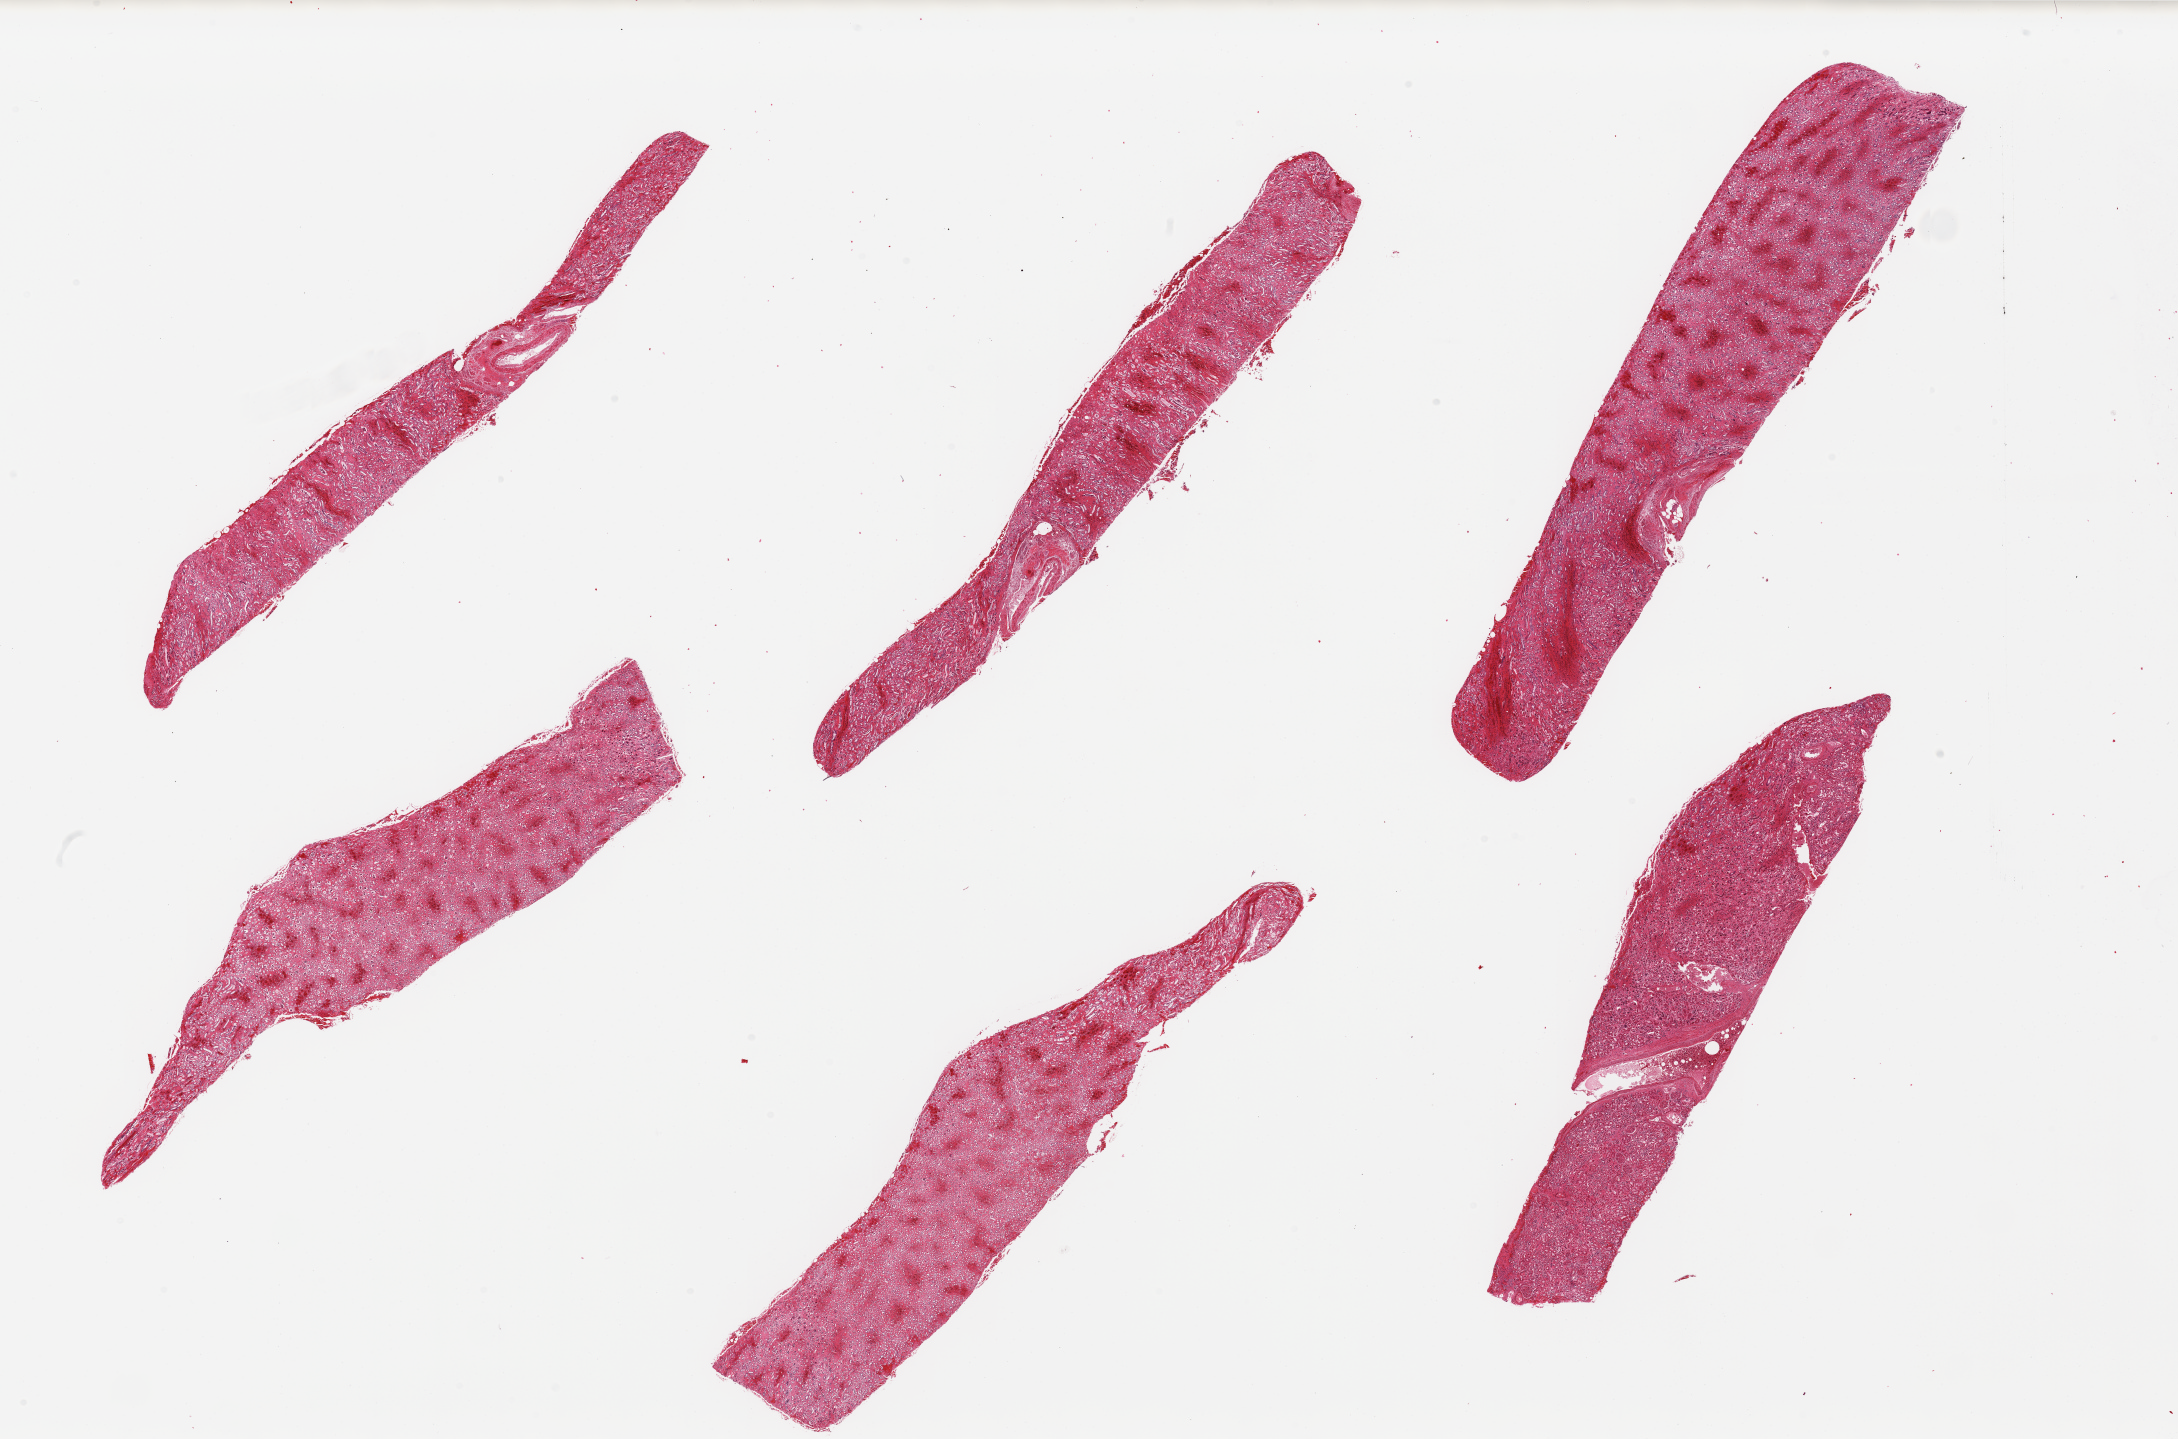
Digitized haematoxylin and eosin-stained section, brightfield, whole scanned area (about 34.5 x 22.8 mm) shown as a low-resolution overview. PAXgene-fixed, paraffin-embedded tissue. Sampled site (target tissue): renal cortex. Donor tissue sample. Male donor.
Review note (as recorded): 6 pieces; 5 and half of 6th are medulla; small cortex sample.